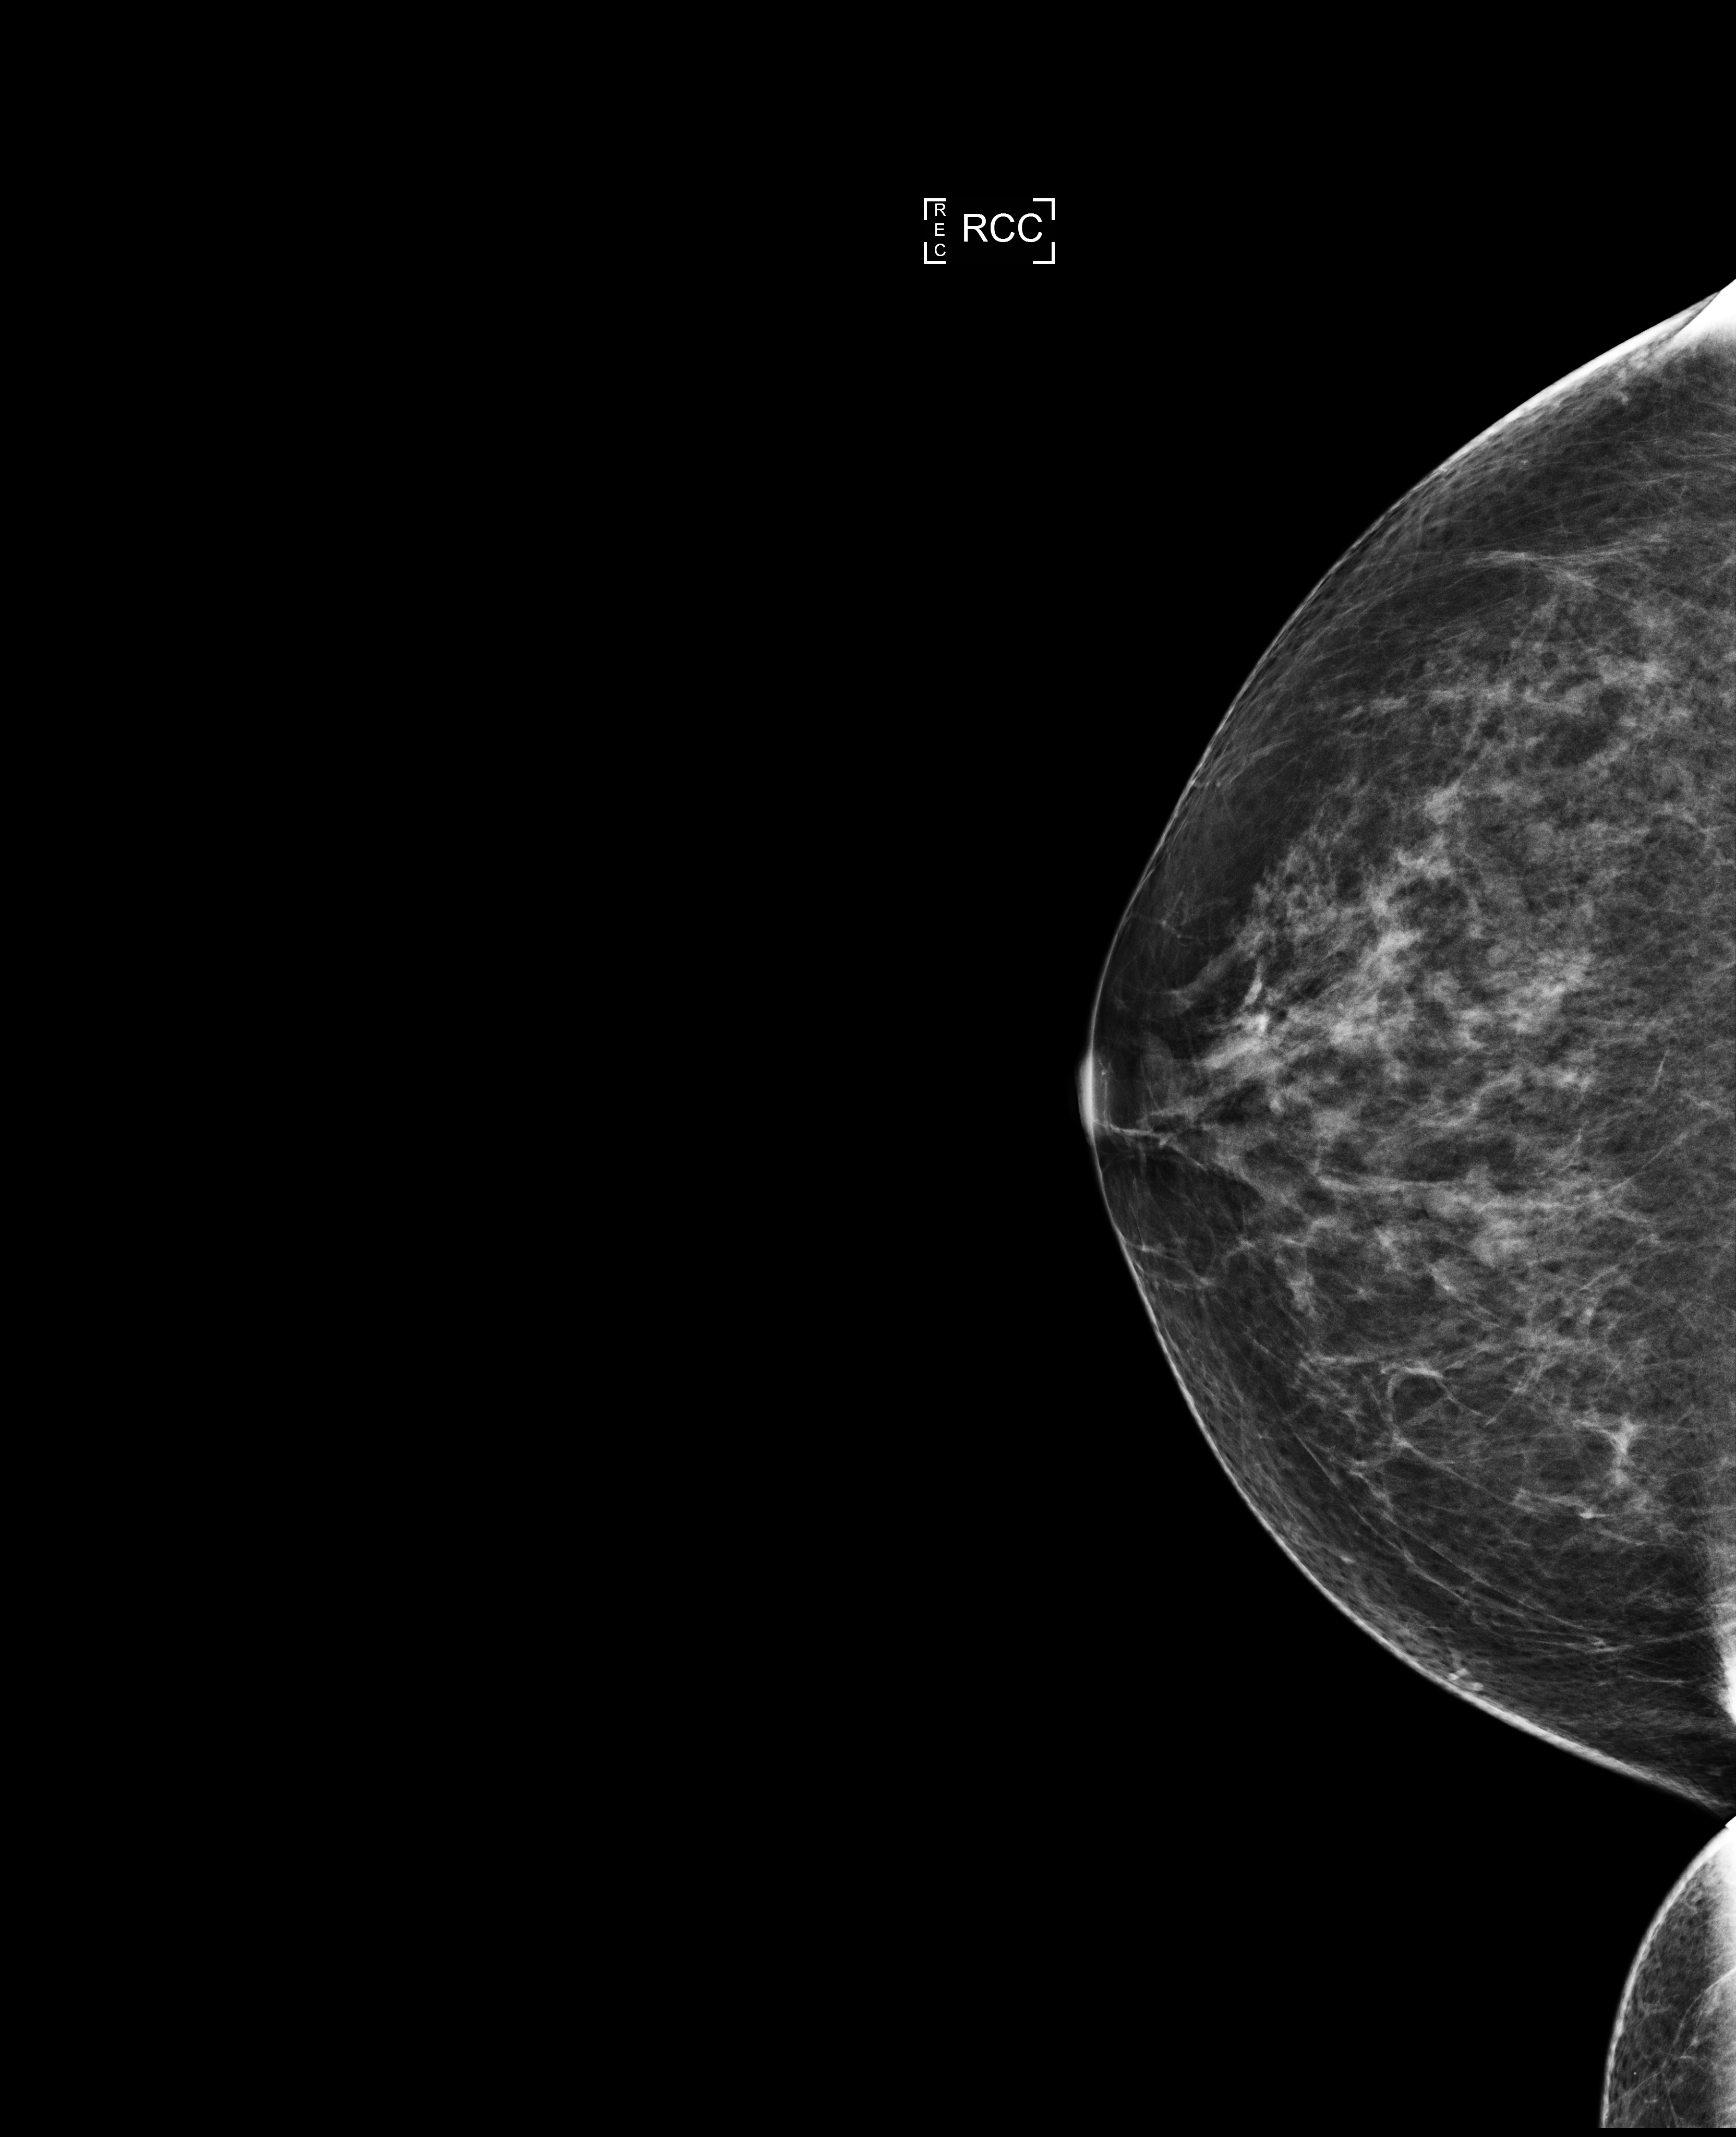
Annual screening mammography examination. Patient aged 53 years (female).
Image type: full-field digital mammogram. Breast: right. Projection: craniocaudal (CC) view.